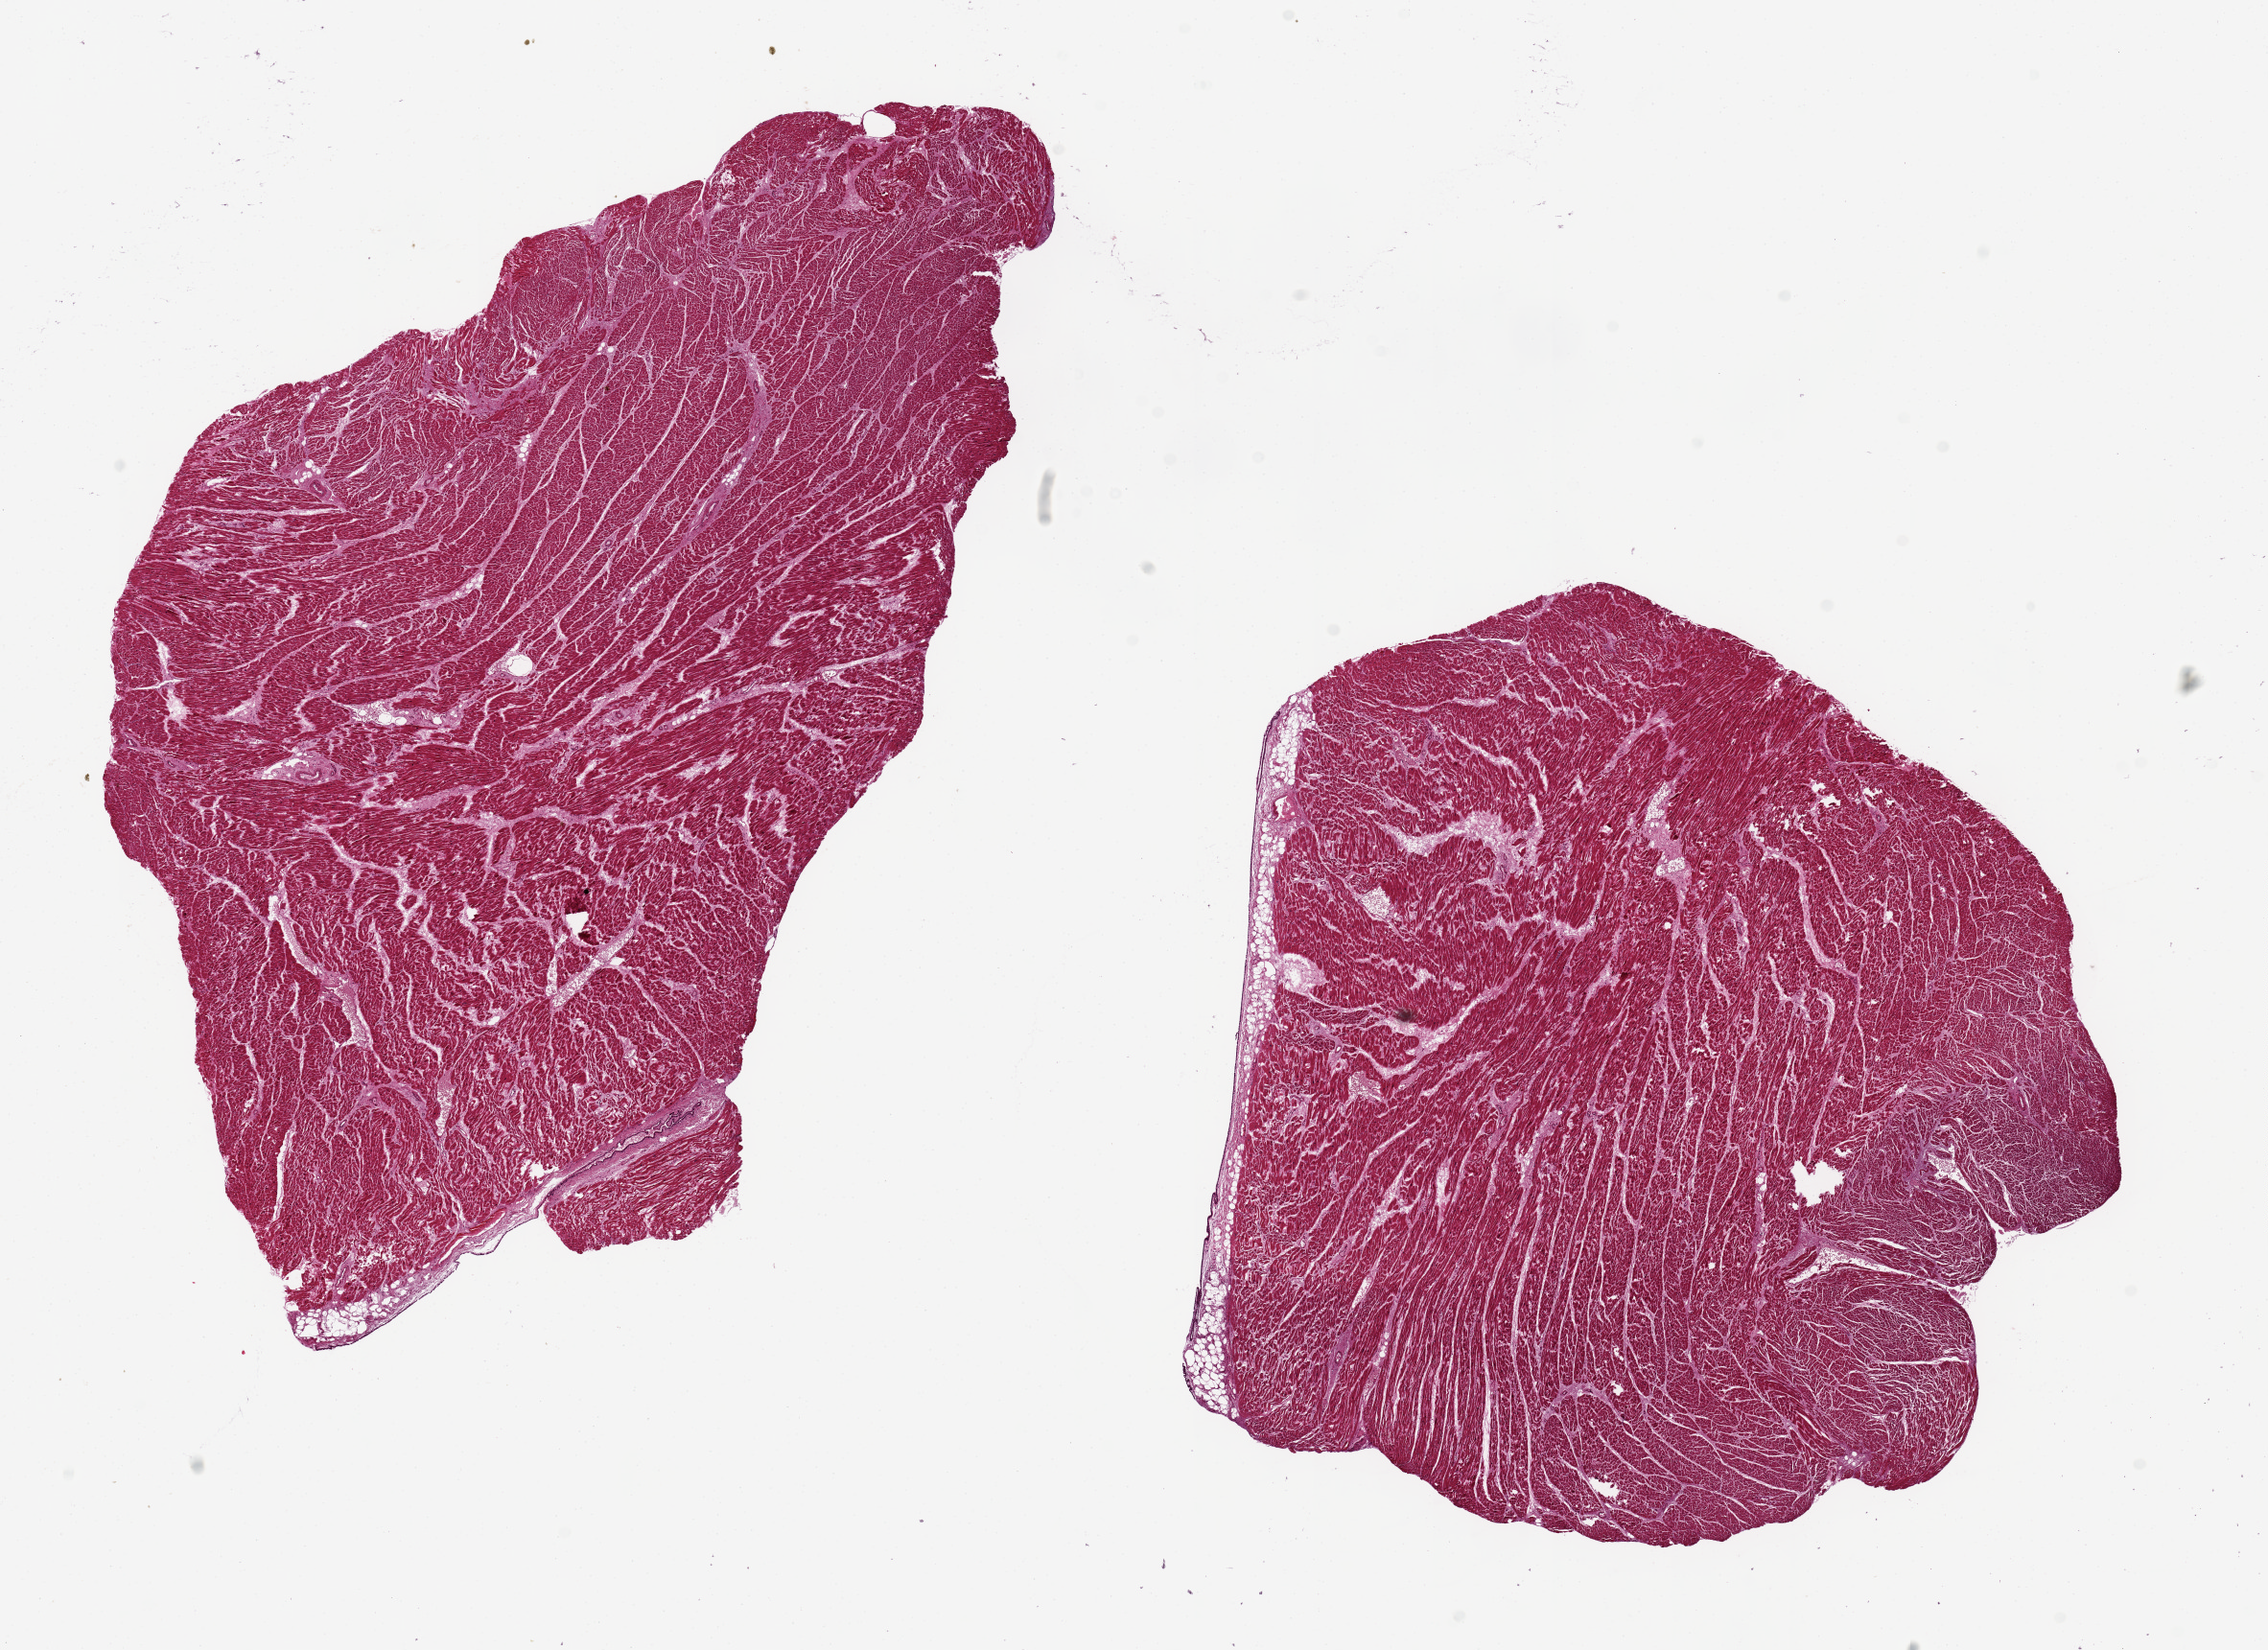
Whole-slide image, H&E stain, shown as a low-resolution overview of the whole scanned area (about 18.7 x 13.6 mm). PAXgene-fixed, paraffin-embedded tissue. Sampled site (target tissue): heart. Donor tissue sample. Donor sex: male.
Review note (as recorded): 2 aliquots, ~8x6mm.